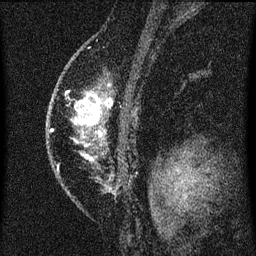
Breast MRI (dynamic contrast-enhanced), one sagittal slice; slice 47 of 60 in the series (ordered by position); dynamic contrast-enhanced series, image 2 of 3 at this slice position (ordered by acquisition); 1.5 T; TE 4.2 ms, TR 8 ms; 256 × 256 image matrix. Female patient, age 46 years.
Outlined on this slice (semi-automatically segmented with operator editing):
- analysis volume of interest (the breast-tissue region the enhancement analysis was run in; not a lesion): bounding box (x1, y1, x2, y2) in pixels: (55, 74, 113, 191)
- tumour enhancement mask (voxels above the 70 % enhancement threshold inside the analysis volume of interest): (74, 94, 112, 157)